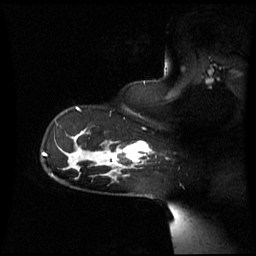
Breast MRI (dynamic contrast-enhanced), one sagittal slice; position 46 of 60 along the scan axis; dynamic contrast-enhanced series, image 2 of 3 at this slice position (ordered by acquisition); 1.5 T; TE 4.2 ms, TR 8.4 ms; 256 × 256 image matrix, field of view 270 × 270 mm. Female patient, age 39 years. From the clinical record (not read from this slice): setting: breast cancer imaged before/during neoadjuvant chemotherapy; receptor status: triple-negative.
Annotated regions visible in this slice (semi-automatic segmentation, software-assisted and operator-edited):
- analysis volume of interest (the breast-tissue region the enhancement analysis was run in; not a lesion): box from (x=101, y=142) to (x=149, y=173) px
- tumour enhancement mask (voxels above the 70 % enhancement threshold inside the analysis volume of interest): (x=107, y=142)–(x=149, y=165)